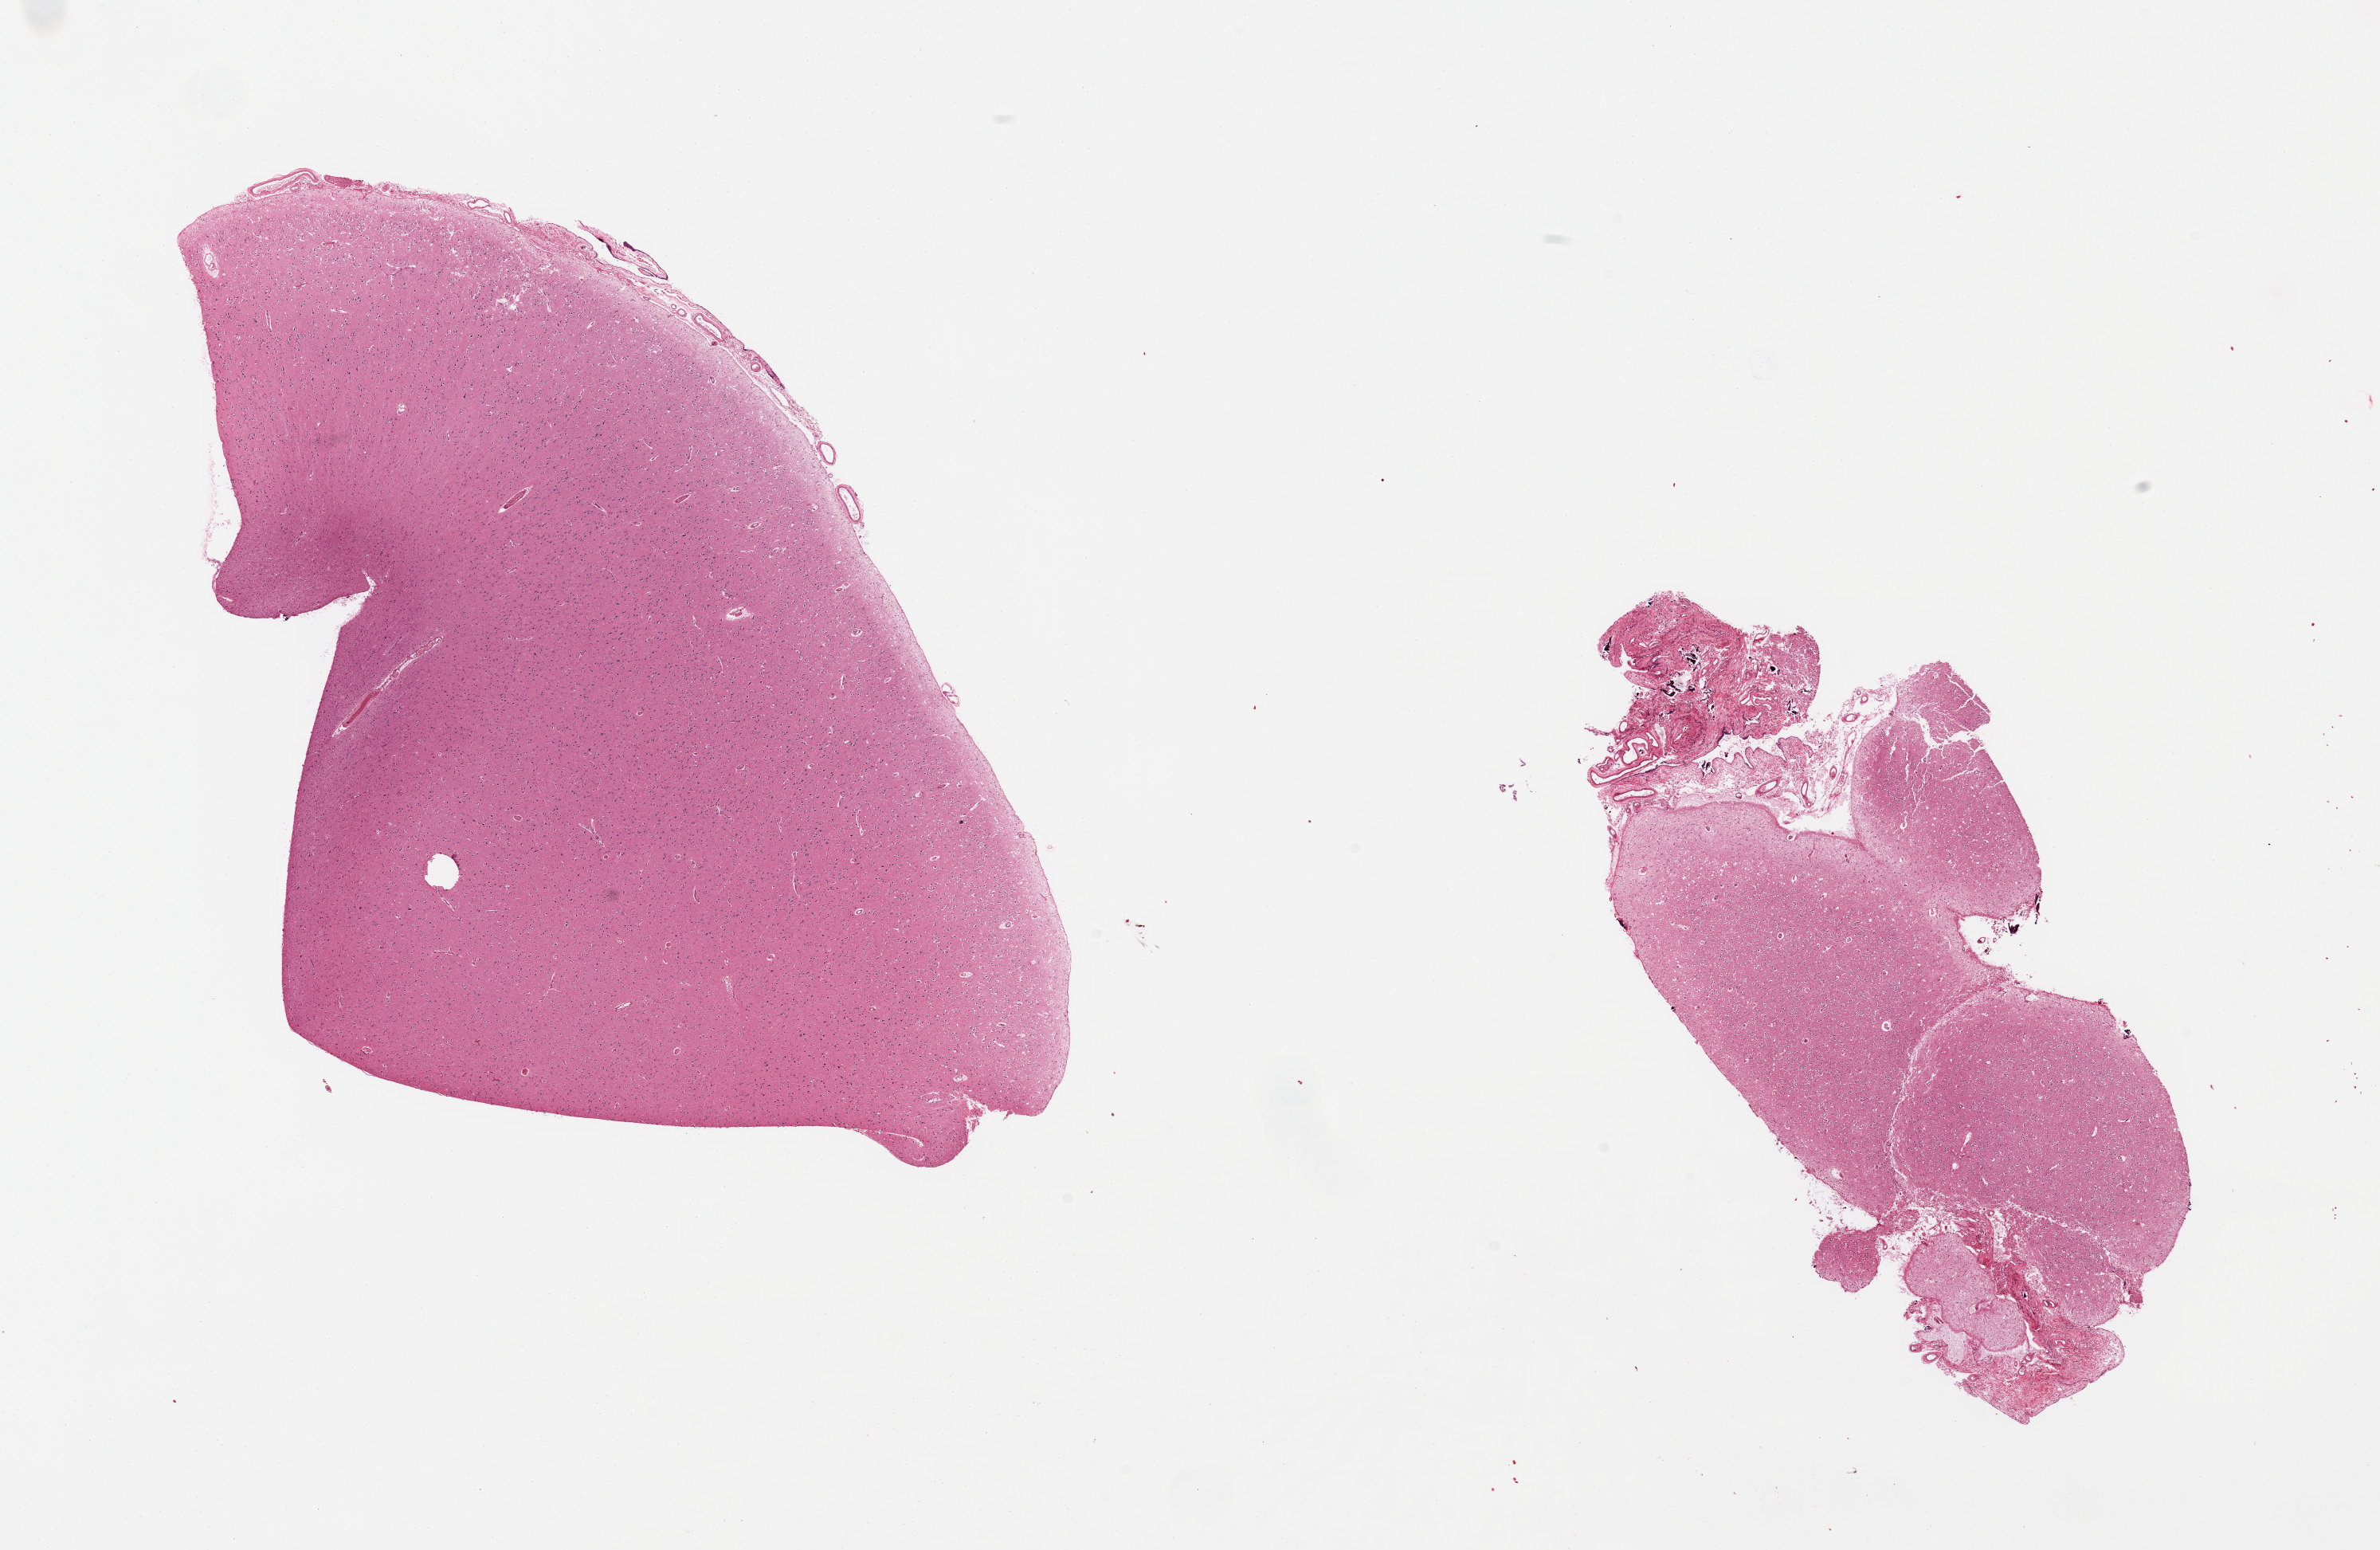
Whole-slide image, haematoxylin and eosin stain — a low-resolution overview of the entire scanned area, about 23.6 x 15.4 mm (from a 20x scan). PAXgene-fixed paraffin-embedded (PFPE) section. Sampled site (target tissue): cerebral cortex. Tissue donor sample.
Pathologist's review note for this sample: 2 pieces, attached portion of meninges.